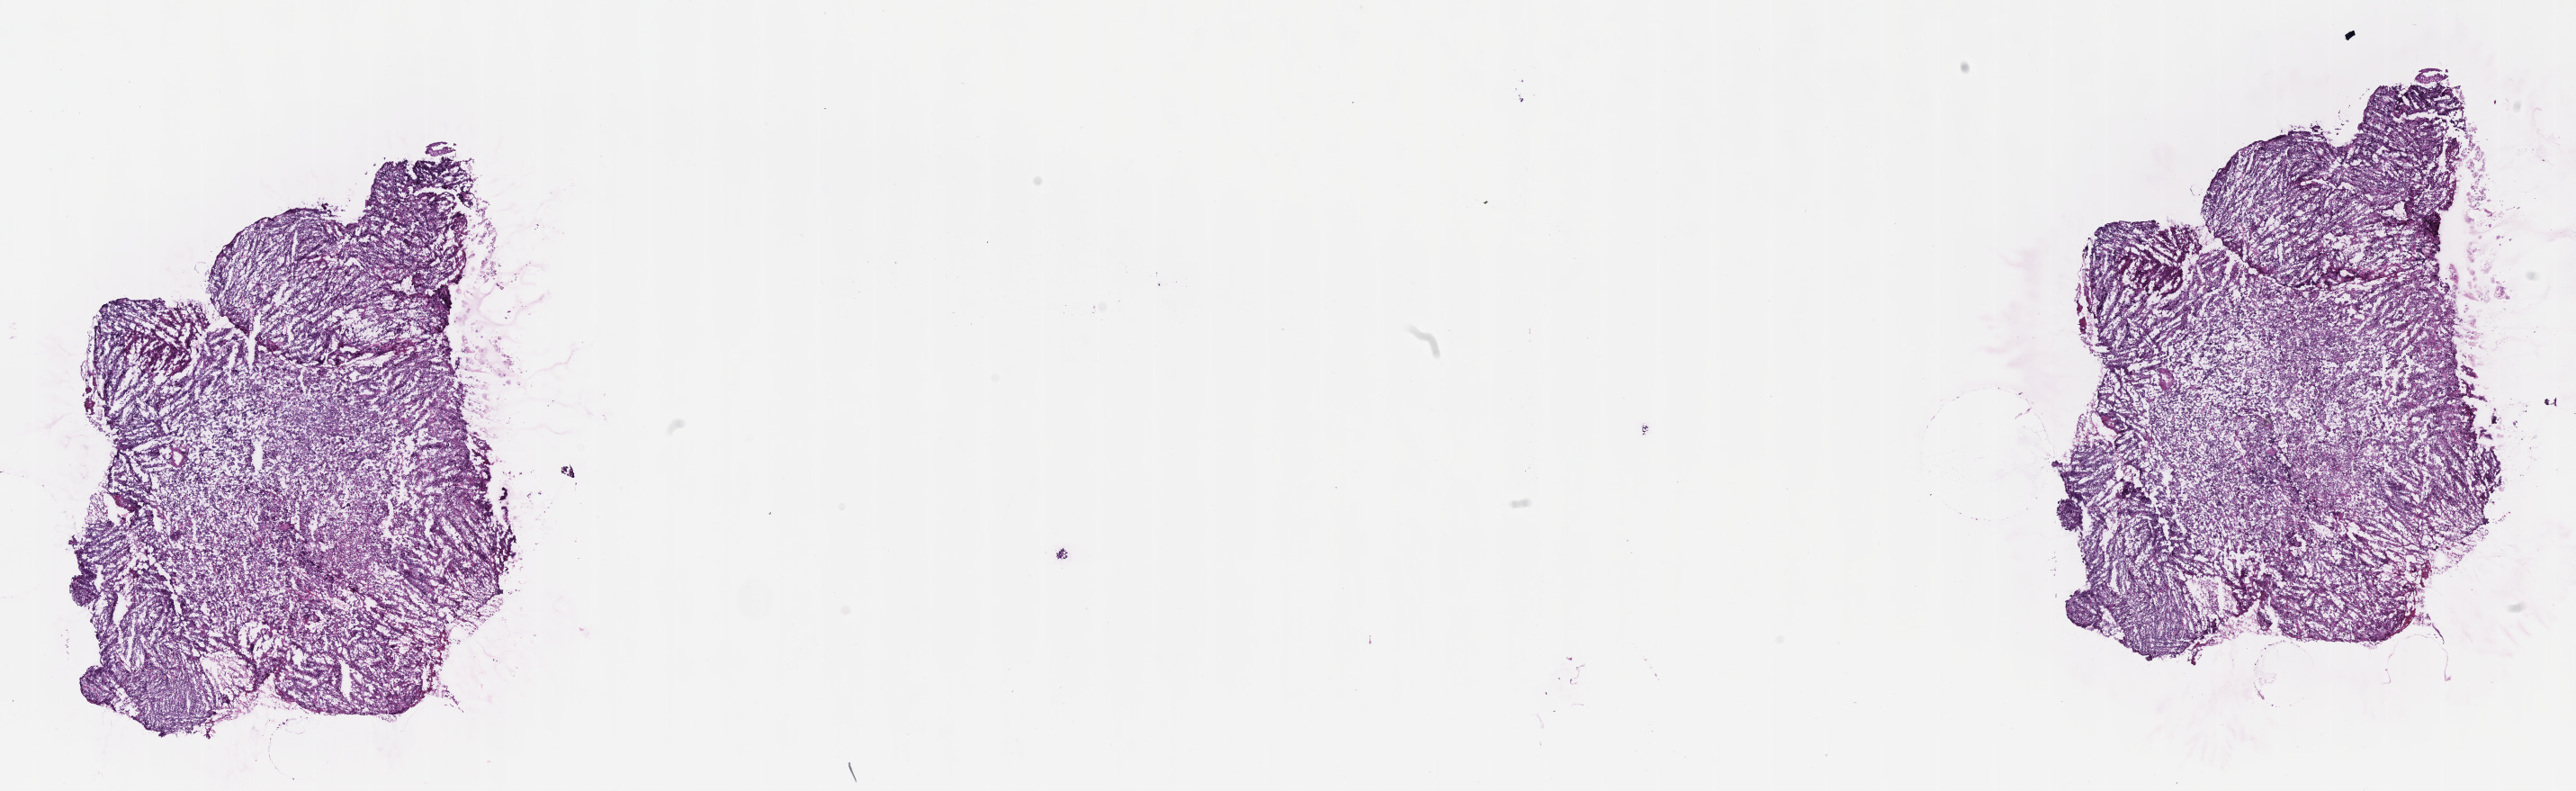
Whole-slide image, haematoxylin and eosin stain — a low-resolution overview of the entire scanned area, about 23.1 x 7.1 mm; cryosection; primary tumor; site: cranium. Male patient; age at initial diagnosis 5 years. Slide review estimates, as recorded: tumor cells 75%, tumor nuclei 80%, stromal cells 10%, necrosis 15%, normal cells 0%. Inflammatory infiltration, as recorded: lymphocyte infiltration 10%, monocyte infiltration 30%, neutrophil infiltration 5%.
Ann Arbor stage (patient): Stage II. Histologic diagnosis: Burkitt lymphoma, NOS.